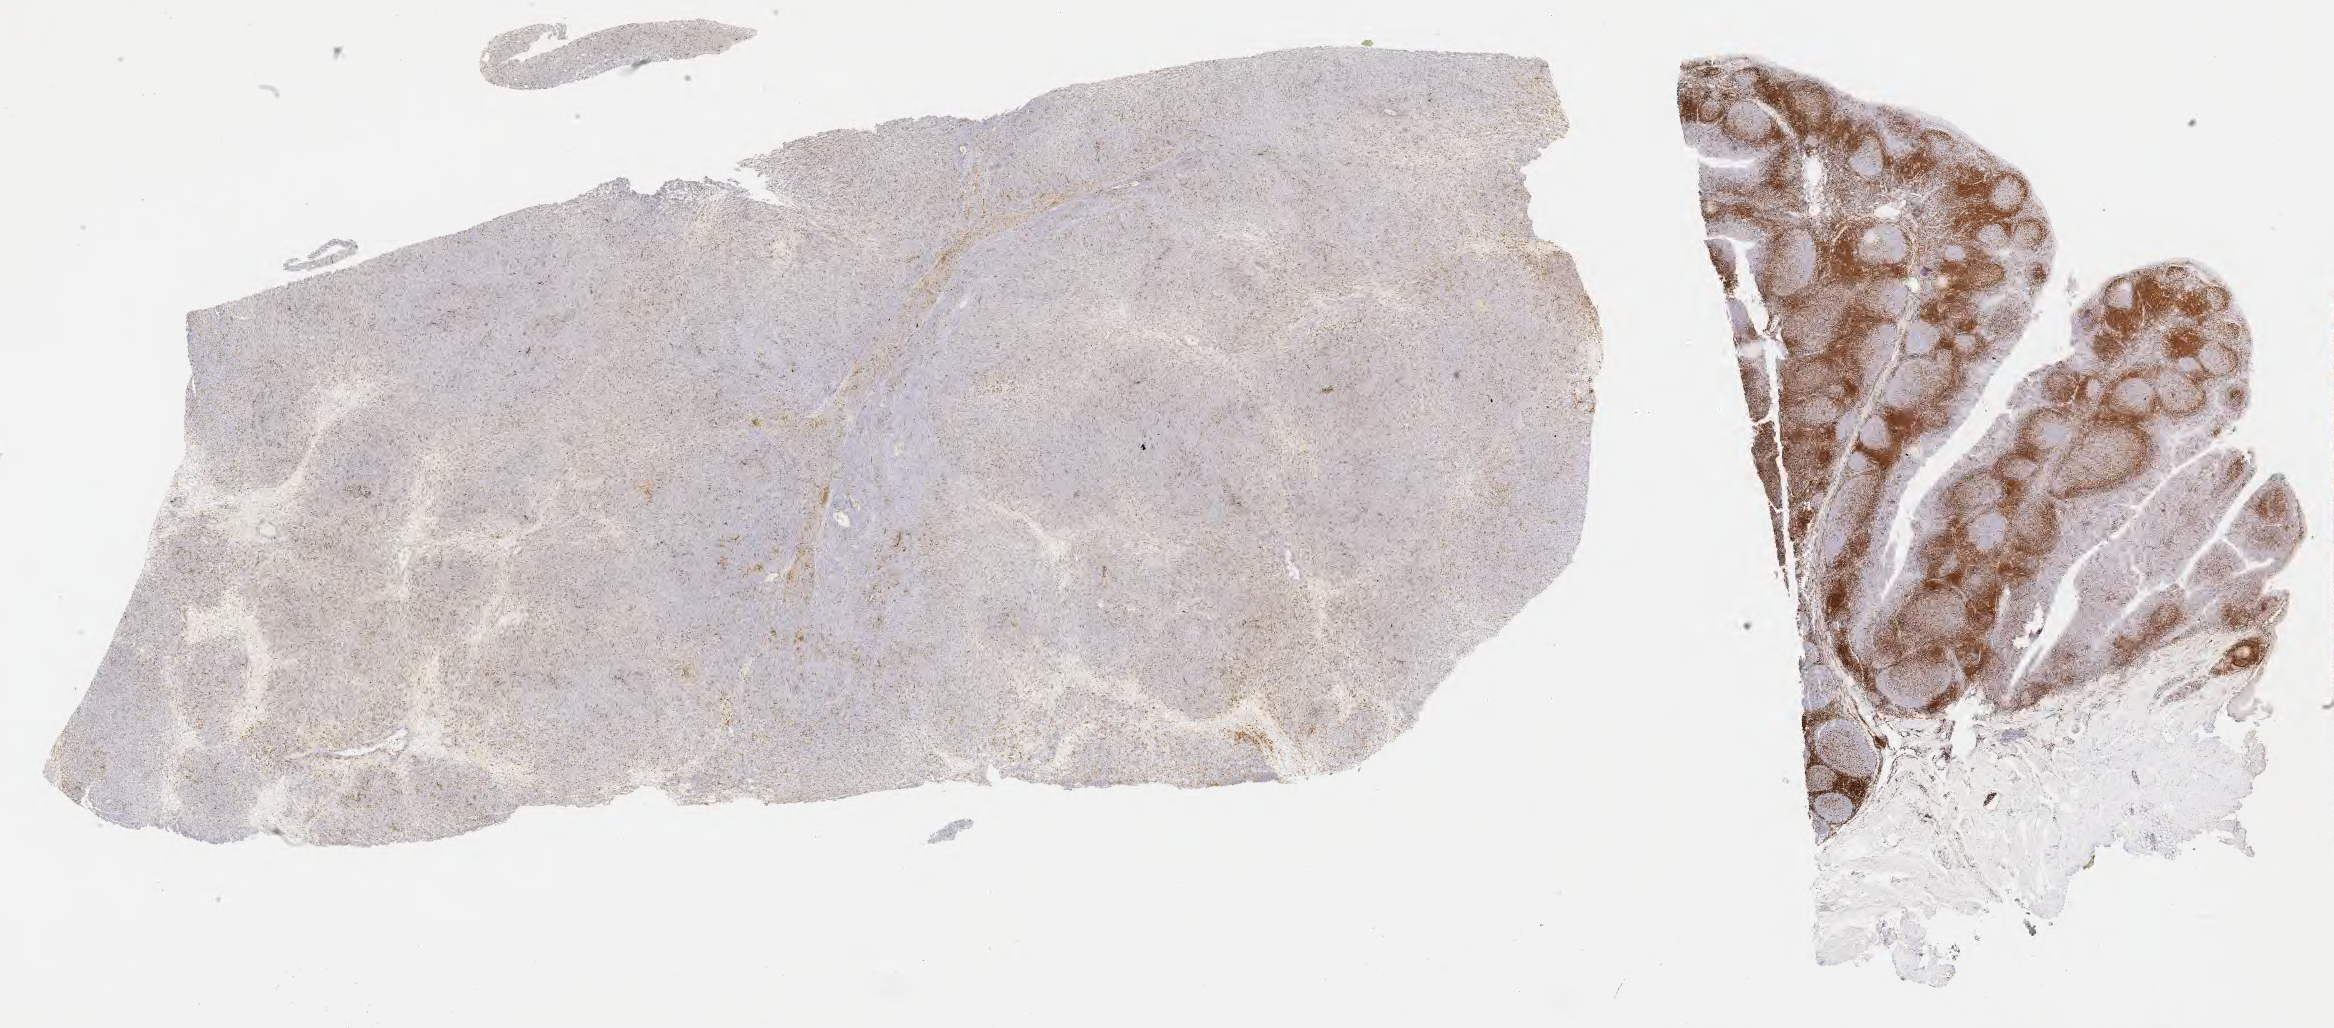
Immunohistochemistry (IHC) whole-slide image stained for CD3, shown as a low-resolution overview of the whole scanned area (about 37.8 x 16.6 mm), specimen: tumor tissue. Patient male; aged 39.
Histologic diagnosis: Diffuse large B-cell lymphoma, NOS.